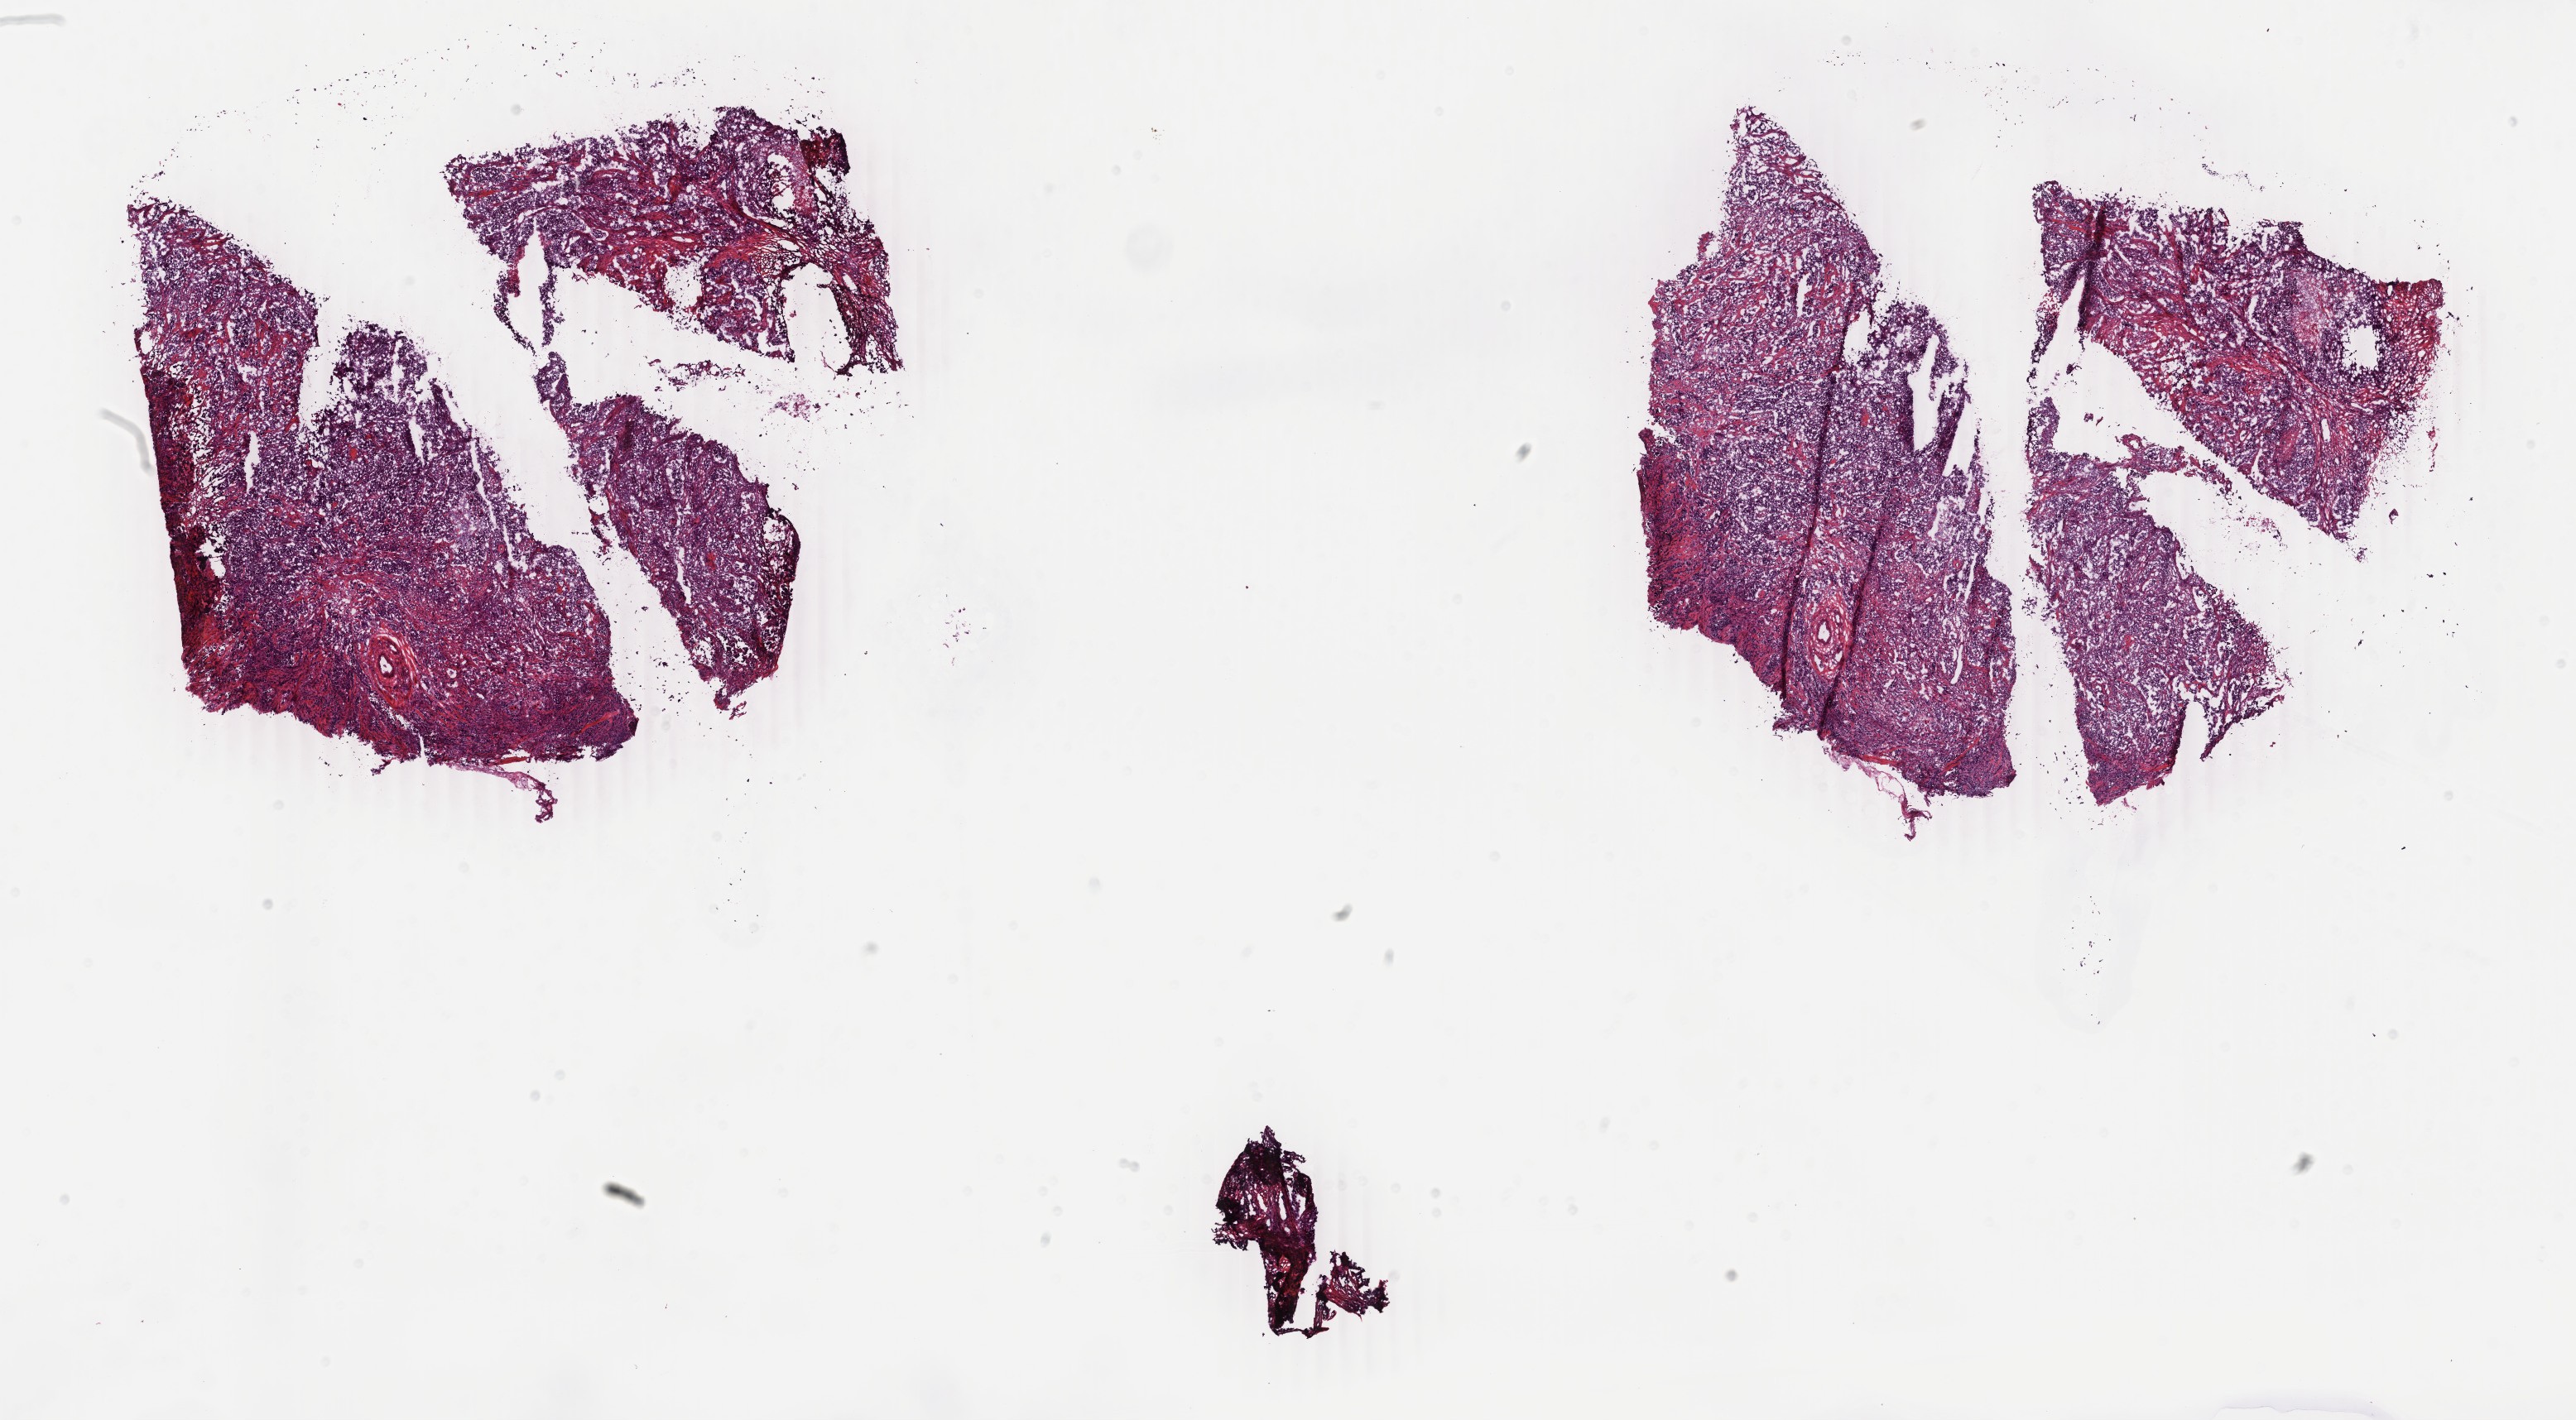
Whole-slide histology image, H&E-stained — shown as a low-resolution overview of the whole scanned area (about 24.7 x 13.6 mm), frozen section, primary tumour sample from the breast. Female, age 38 years at initial diagnosis. Pathologist review of this section (percent, as recorded): tumour cells 75%, tumour nuclei 85%, normal cells 0%, stromal cells 20%, necrosis 5%. Inflammatory infiltration, as recorded: lymphocyte infiltration 0%, monocyte infiltration 0%, neutrophil infiltration 0%.
Lymph nodes positive (case pathology): 0 of 15 examined. Laterality: left. AJCC pathologic stage: IIA. TNM: T2 N0 (i-) M0. Diagnosis: Infiltrating duct carcinoma, NOS.